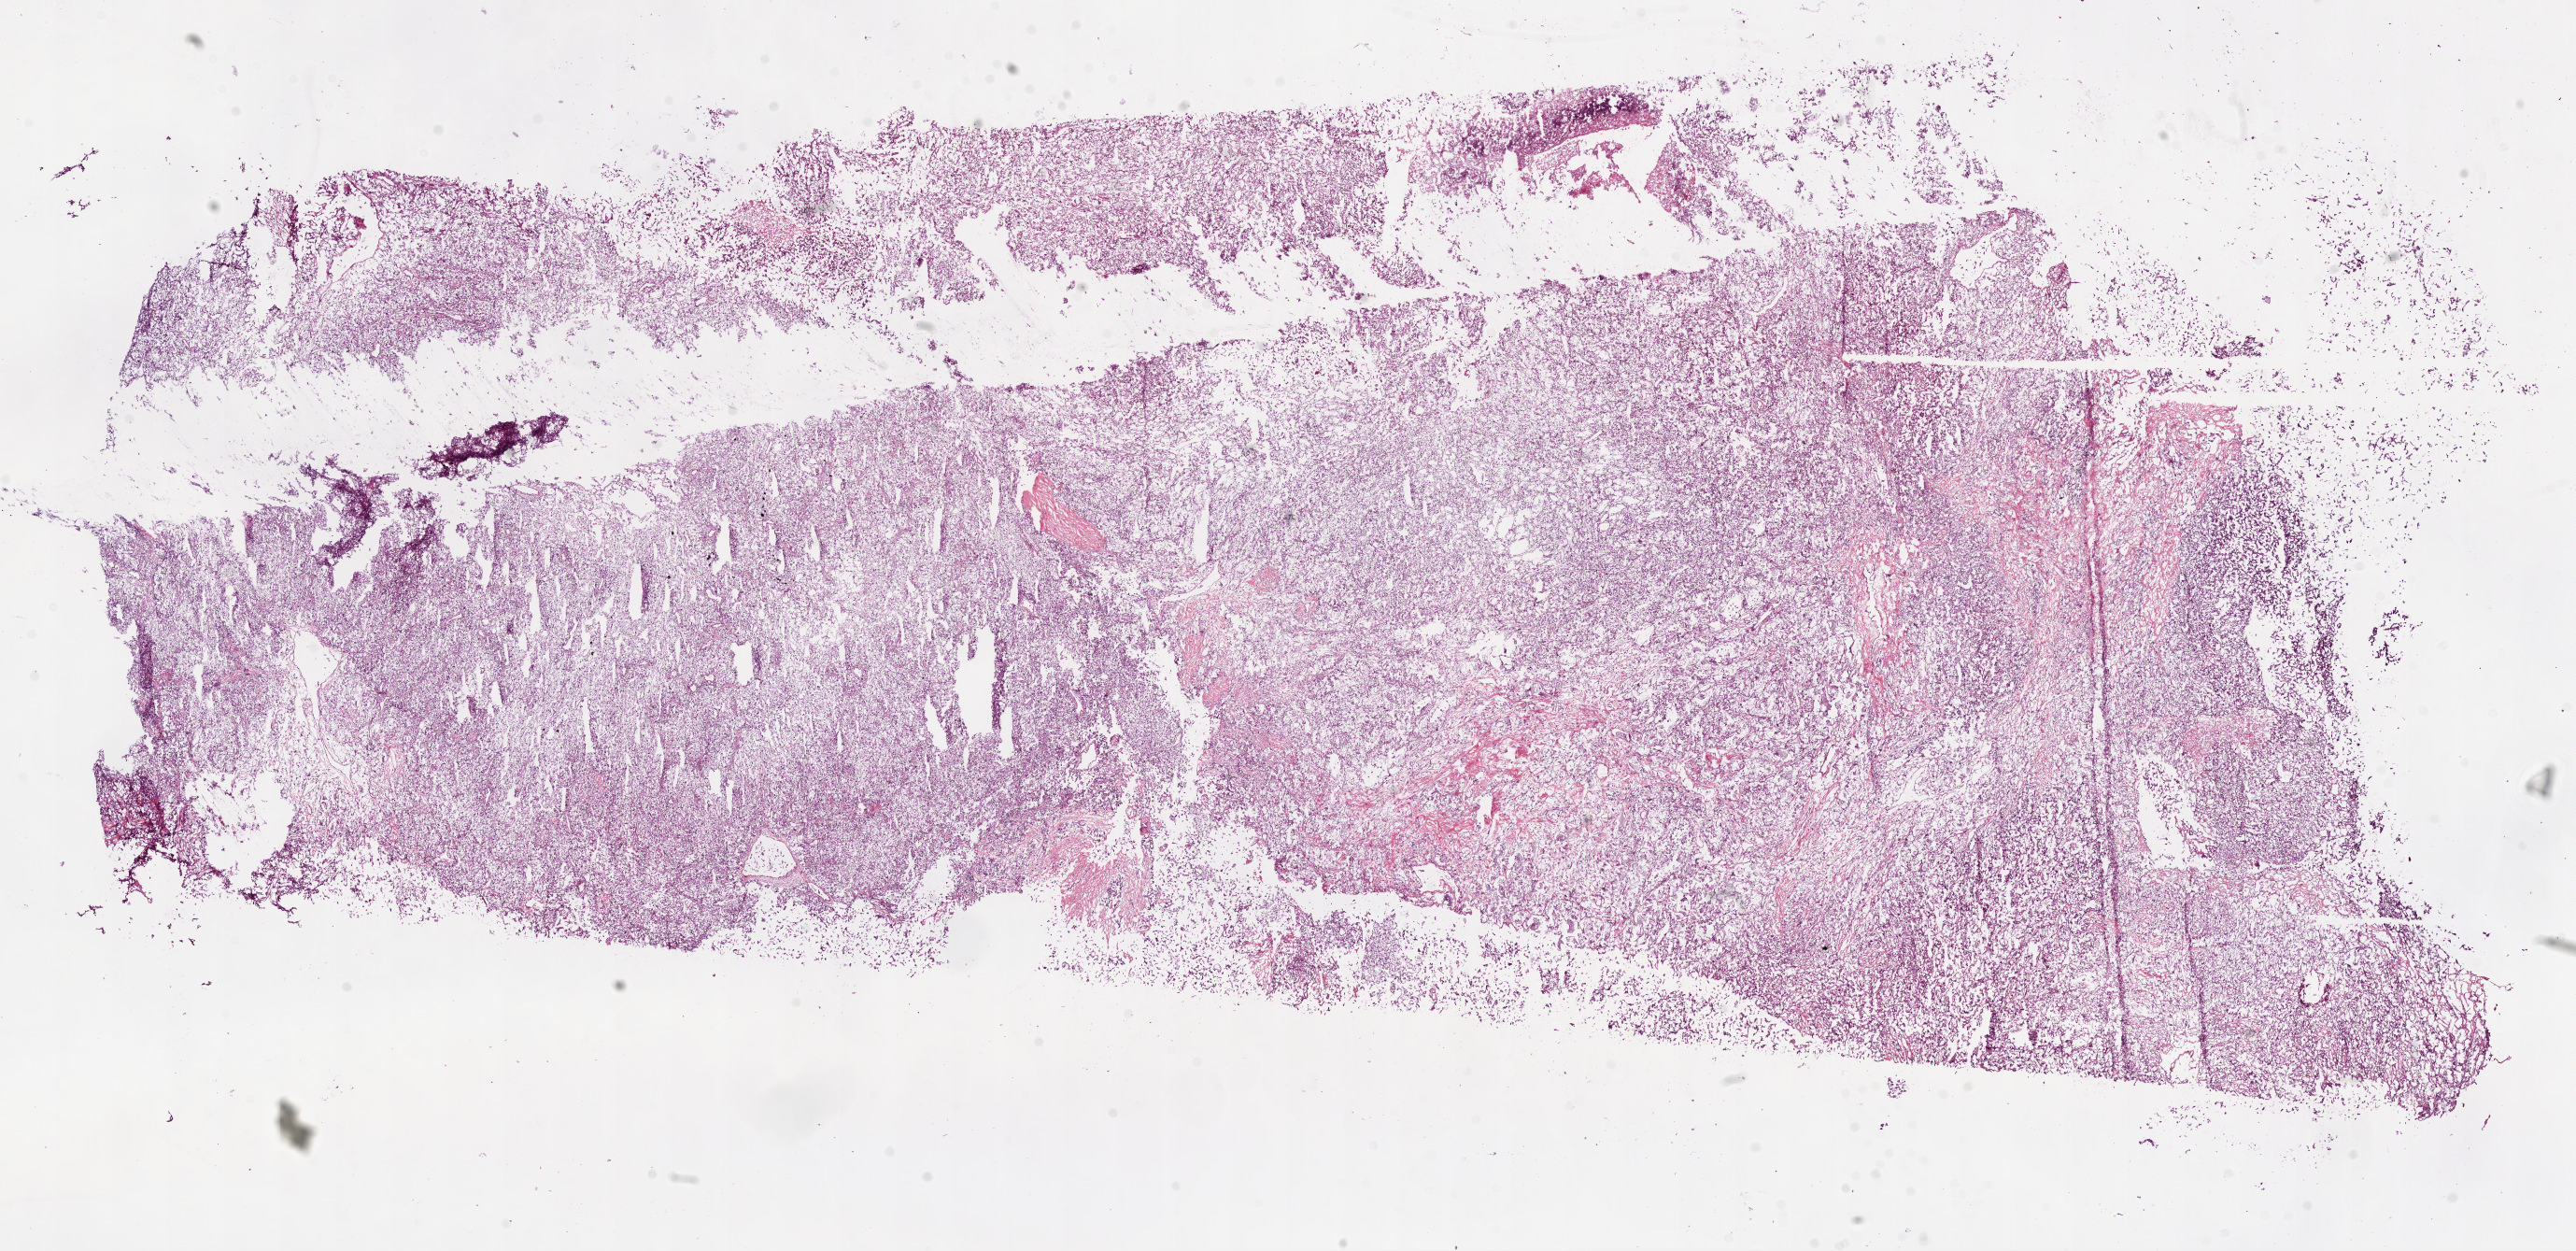
Digitized Hematoxylin and eosin (H&E) stained tissue section (whole slide), whole scanned area (about 22.2 x 10.8 mm) shown as a low-resolution overview, frozen section, primary tumour sample from the kidney. Patient: male, age at initial diagnosis 73 years. Histologic grade: G4 (undifferentiated). Composition of this section per pathologist review: tumour cells 87%, tumour nuclei 85%, normal cells 0%, stromal cells 10%, necrosis 3%.
Pathologic diagnosis: Clear cell adenocarcinoma, NOS. Laterality: left. AJCC pathologic stage: III.